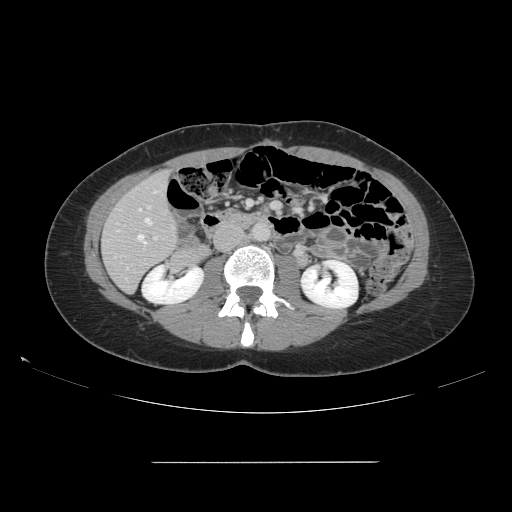
Contrast-enhanced abdominal CT, one axial slice. Position 53 of 151 along the scan axis. 120 kVp. Soft-tissue window (W 400 / L 40 HU). 512 × 512 image matrix. Female patient, age 46 years. Case-level facts recorded for this patient, not image findings: diagnosis: colorectal cancer liver metastases, imaged before liver resection; multiple liver metastases: yes; largest metastasis: 3 cm; disease in both lobes: yes.
Structures marked on this image (manually delineated by an expert):
- hepatic veins: bounding box [x1, y1, x2, y2] px = [138, 218, 152, 240]
- liver: [103, 172, 178, 292]
- planned liver remnant (the part of the liver to remain after resection): [103, 172, 178, 292]
- portal vein (with intrahepatic branches): [154, 237, 157, 239]